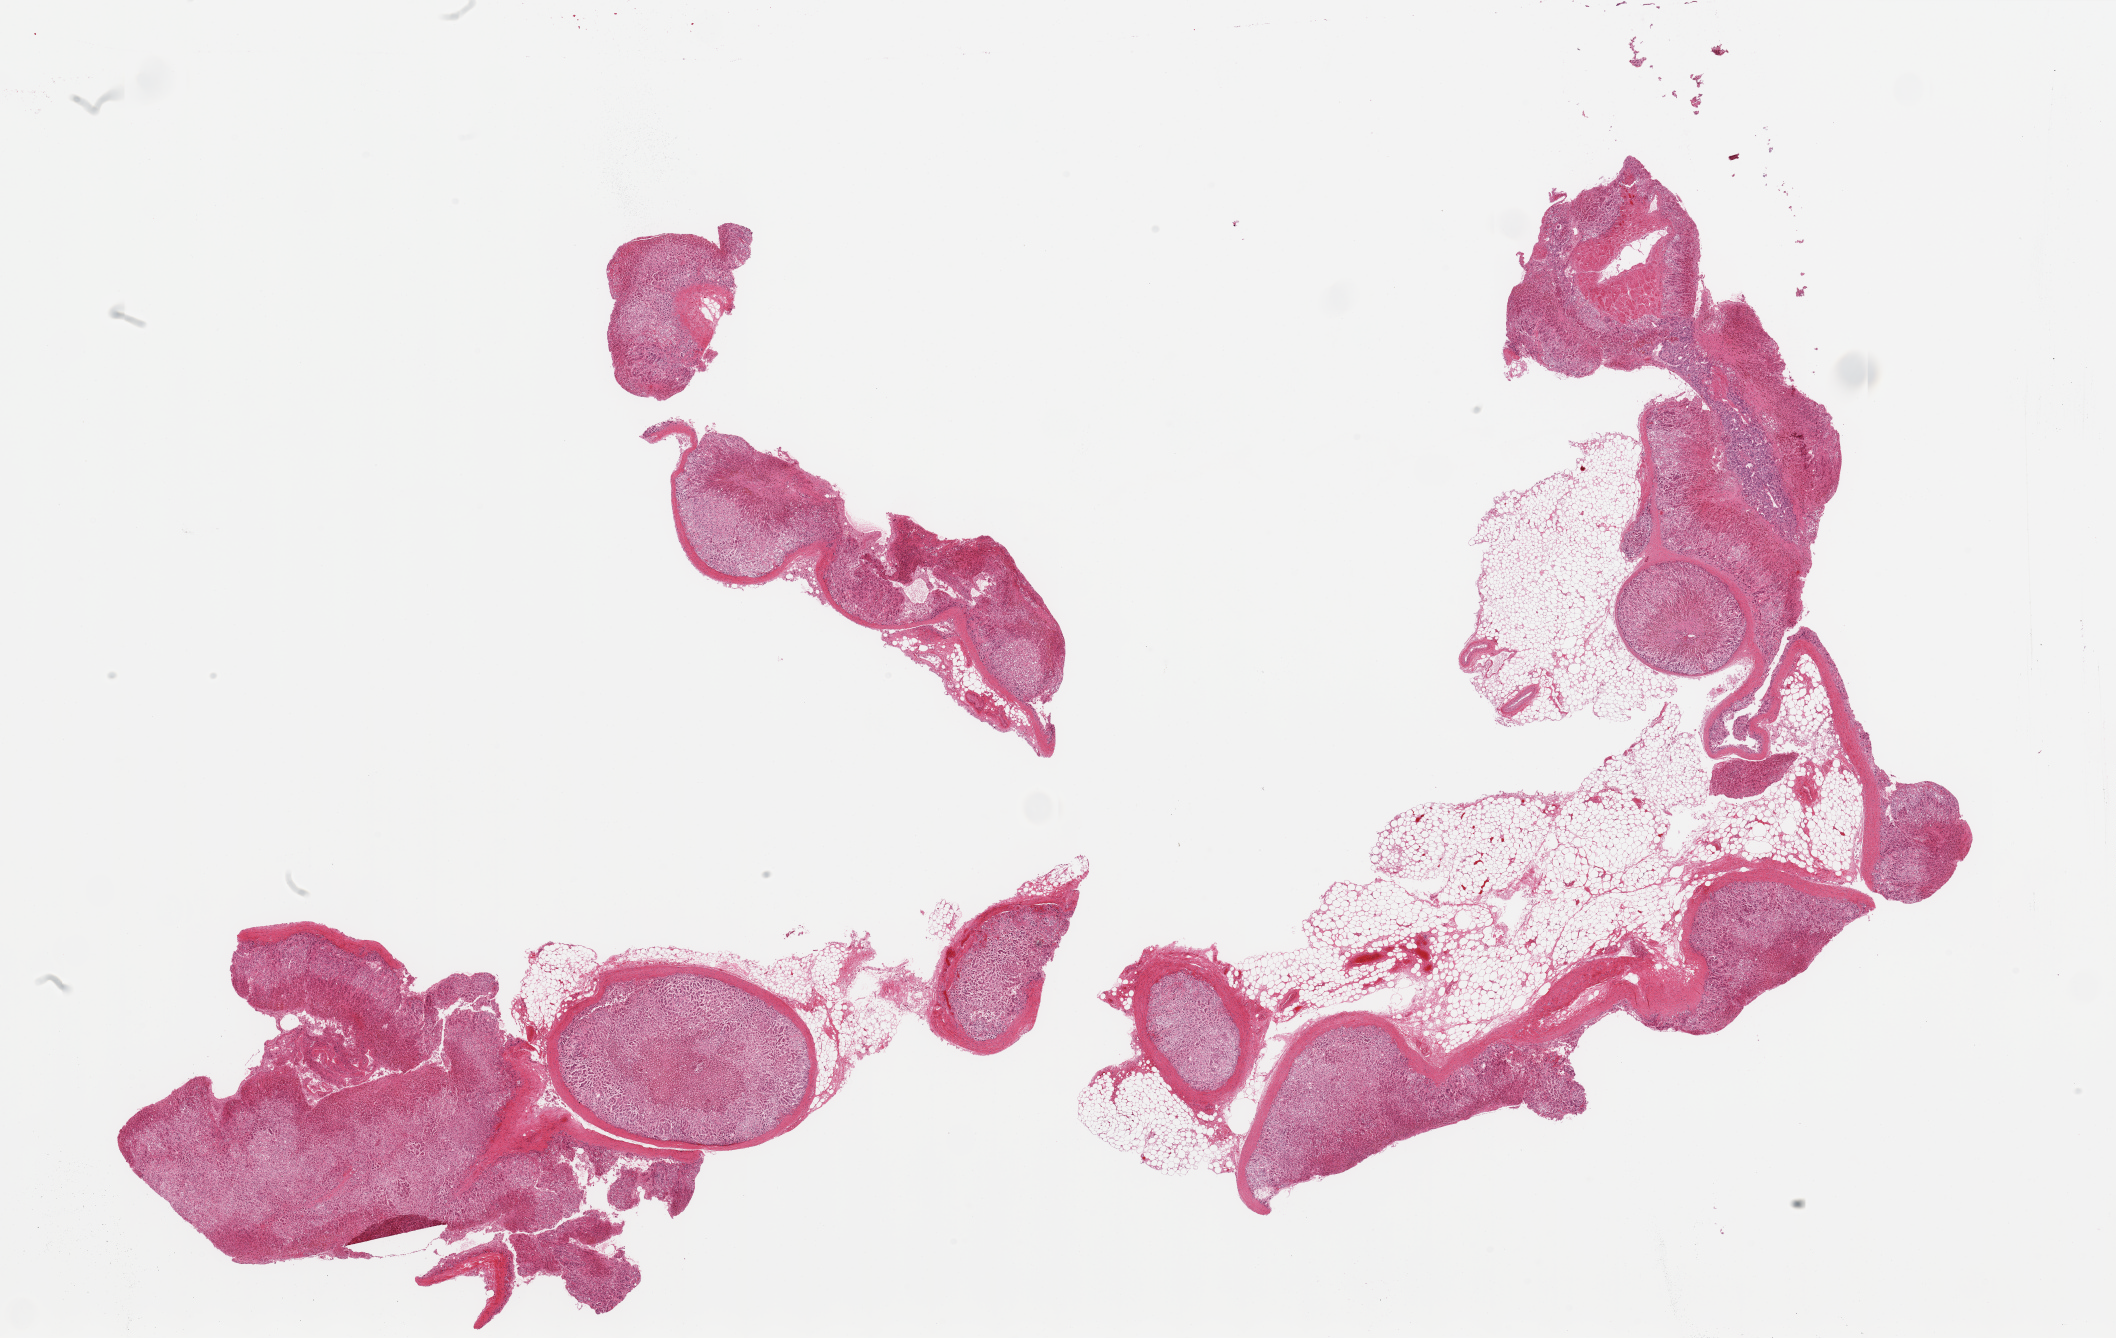
Digitized H&E-stained section — a low-resolution overview of the entire scanned area, about 33.5 x 21.2 mm; PAXgene-fixed paraffin-embedded (PFPE) section; sampled site (target tissue): adrenal gland; tissue donor sample. Donor sex: male.
Pathologist's review note for this sample: 2 pieces, mainly cortex, trace 3mm focus of medulla; 30% adherent fat; moderately advanced autolysis.